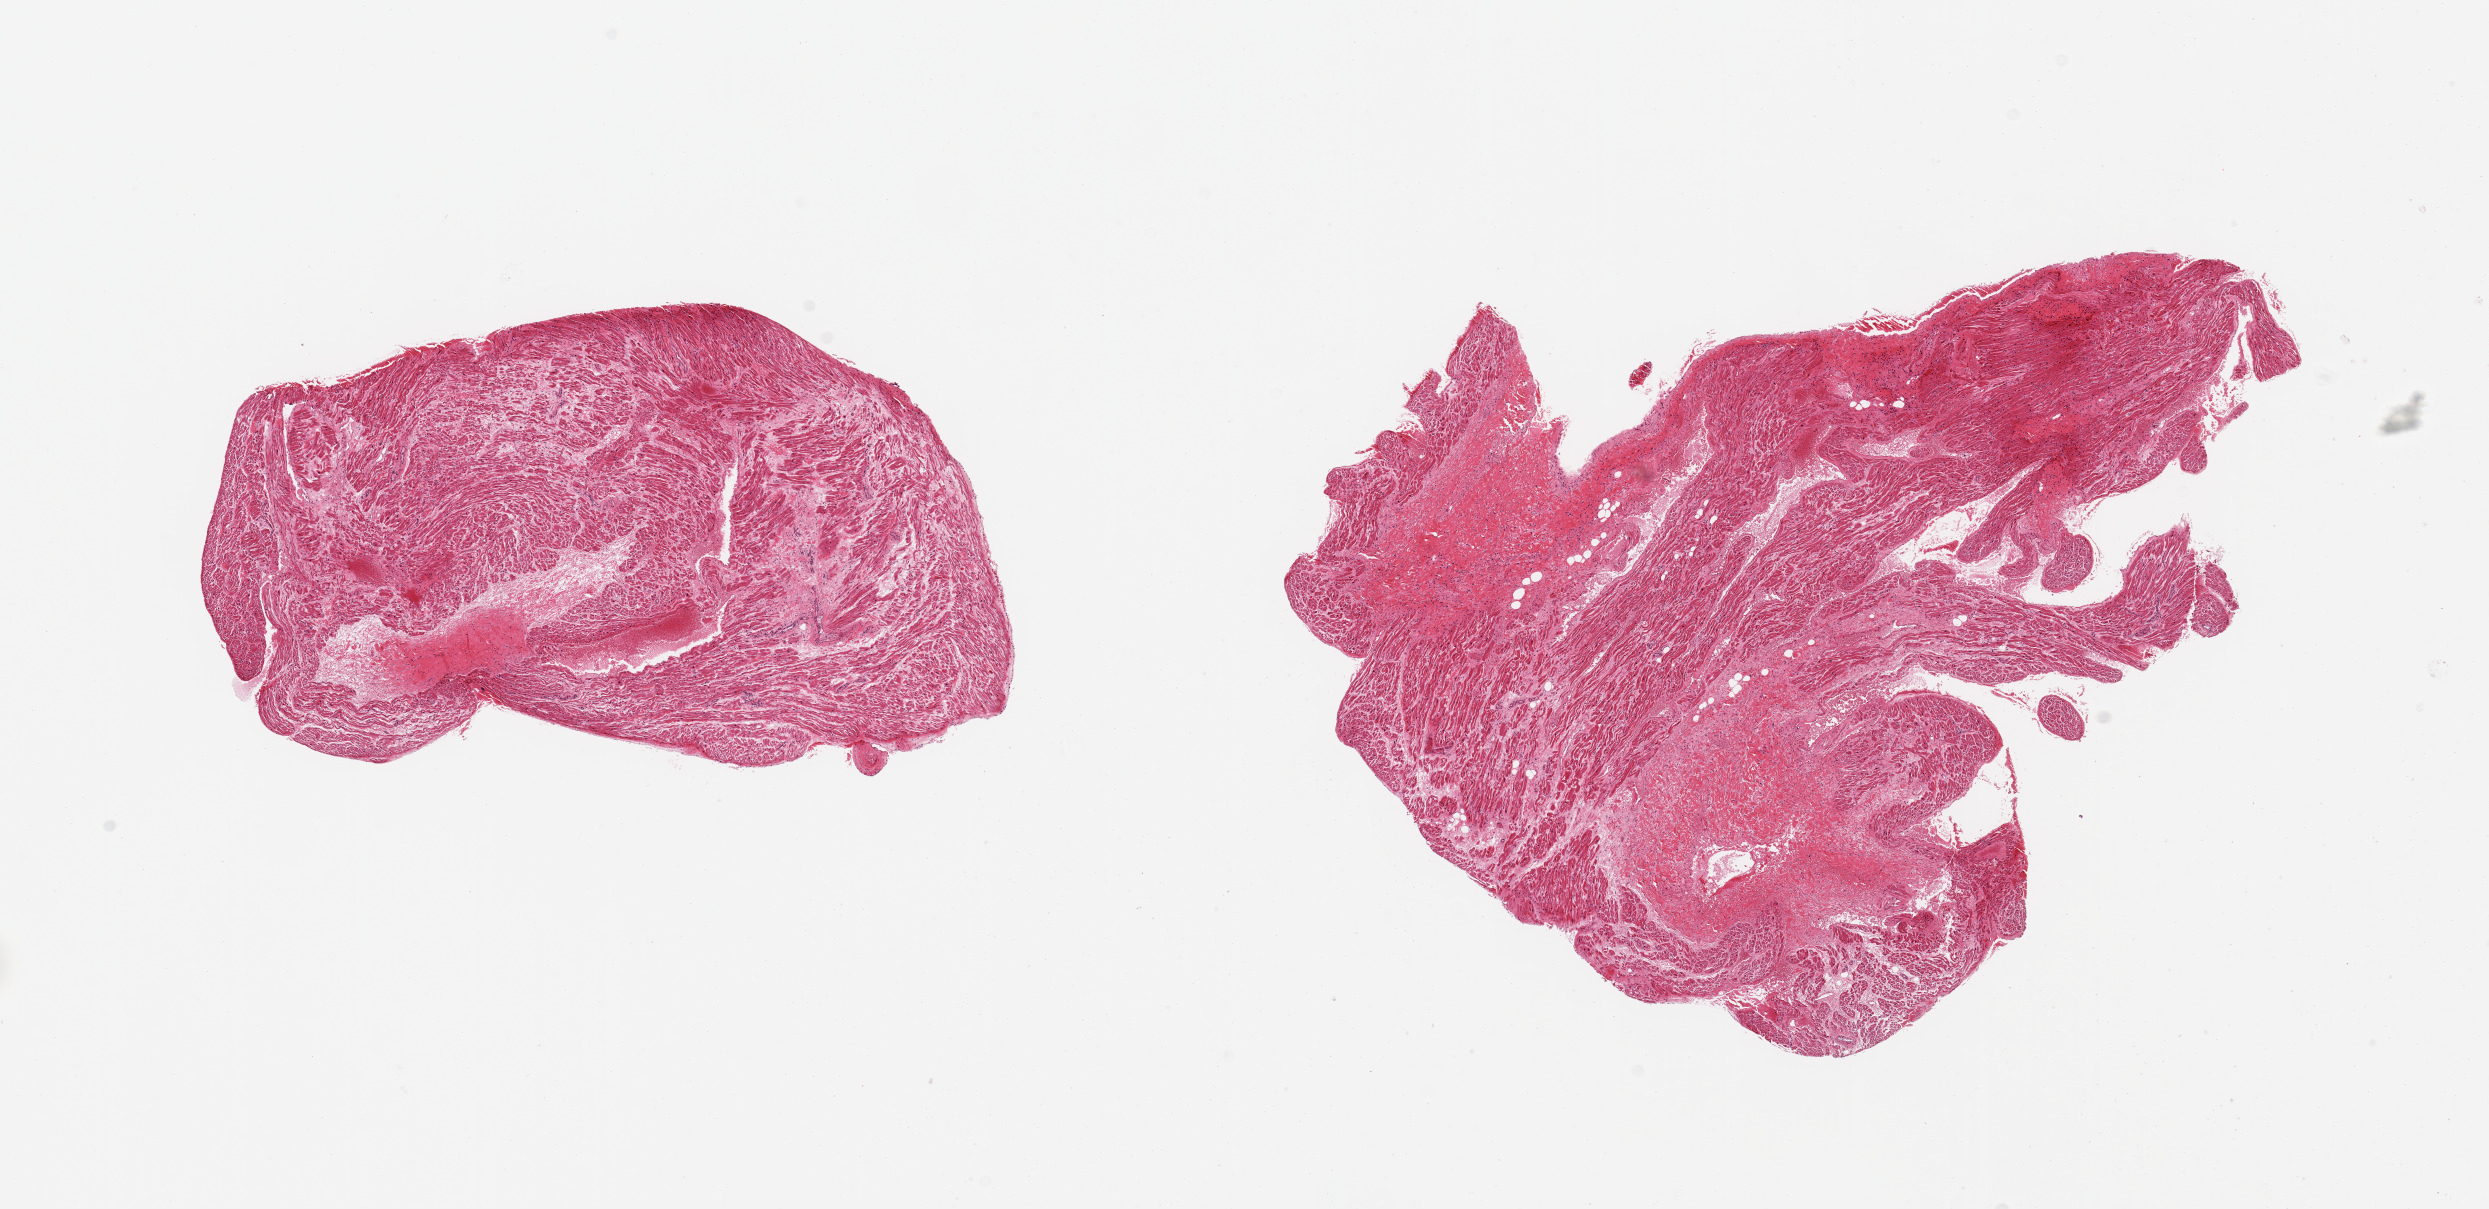
Haematoxylin and eosin whole-slide image — whole scanned area (about 19.7 x 9.6 mm, slide scanned at 20x) shown as a low-resolution overview, PAXgene-fixed, paraffin-embedded tissue, sampled site (target tissue): auricular appendage, tissue donor sample.
Review note (as recorded): 2 pieces; 30 & 10% fibrous content.